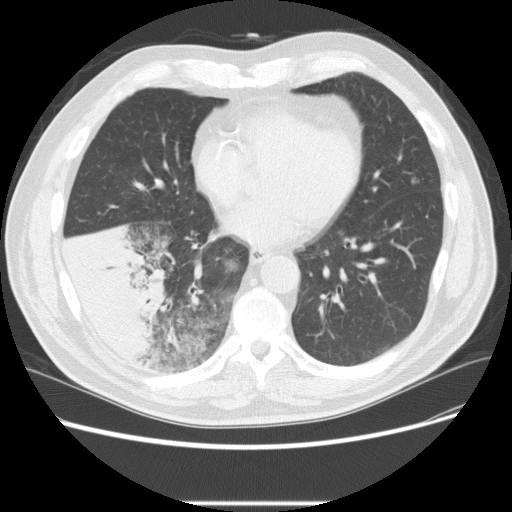
Low-dose screening chest CT, one axial slice. Slice 91 of 233 in the series (ordered by position). Reconstruction kernel STANDARD. 120 kVp. Lung window (W 1500 / L -600 HU). 2.5 mm slice thickness. 512 × 512 image matrix, field of view 380 × 380 mm.
Structures marked on this image (outlined manually by an expert reader):
- lesion 3 (tumor, lower lobe of right lung): box from (x=65, y=223) to (x=170, y=351) px